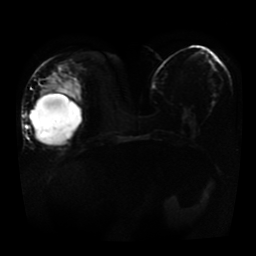
Breast MRI, one axial slice. Slice 15 of 41 in the series (ordered by position). Diffusion-weighted series; image 2 of 4 stored at this slice position (different b-values; order by instance number). 1.5 T. 5 mm slice thickness. 256 × 256 image matrix, field of view 360 × 360 mm. Female patient.
Structures marked on this image (expert manual segmentation):
- tumour on diffusion-weighted imaging: bounding box <55,81,78,98> (left, top, right, bottom; pixels)